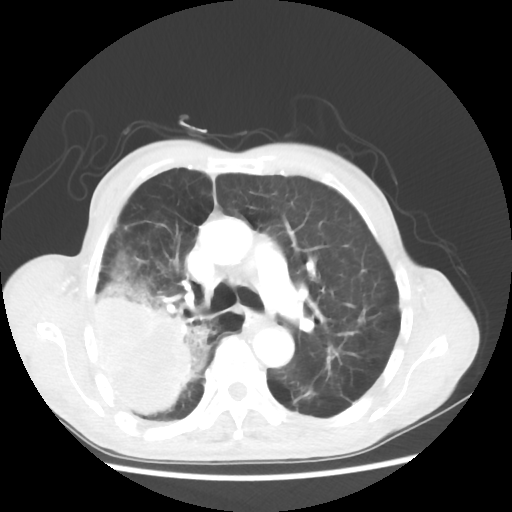
Chest CT, one axial slice. Slice 35 of 58 in the series (ordered by position). Reconstruction kernel STANDARD. Lung window (W 1500 / L -600 HU). 512 × 512 image matrix, field of view 351 × 351 mm. Male patient, age 75 years. From the clinical record (not read from this slice): clinical TNM (as recorded): T4 N1 M1.
Outlined on this slice (rectangle marked by the reading radiologist):
- lung tumour (recorded histology: adenocarcinoma): bounding box (x1, y1, x2, y2) in pixels: (95, 265, 211, 418)